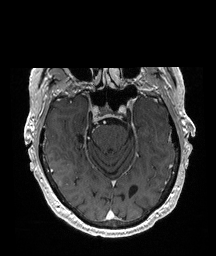
Brain MRI from a brain-tumour surgery series, one axial slice. Position 140 of 208 along the scan axis. T1-weighted post-contrast. 1 mm slice thickness. 216 × 256 image matrix, field of view 216 × 256 mm. Case-level facts recorded for this patient, not image findings: histopathology: Glioblastoma; WHO grade: 4; IDH mutation: no; tumour location: Right Temporal.
Outlined on this slice (outlined manually by an expert reader):
- tumour: bounding box <49,155,70,185> (left, top, right, bottom; pixels)